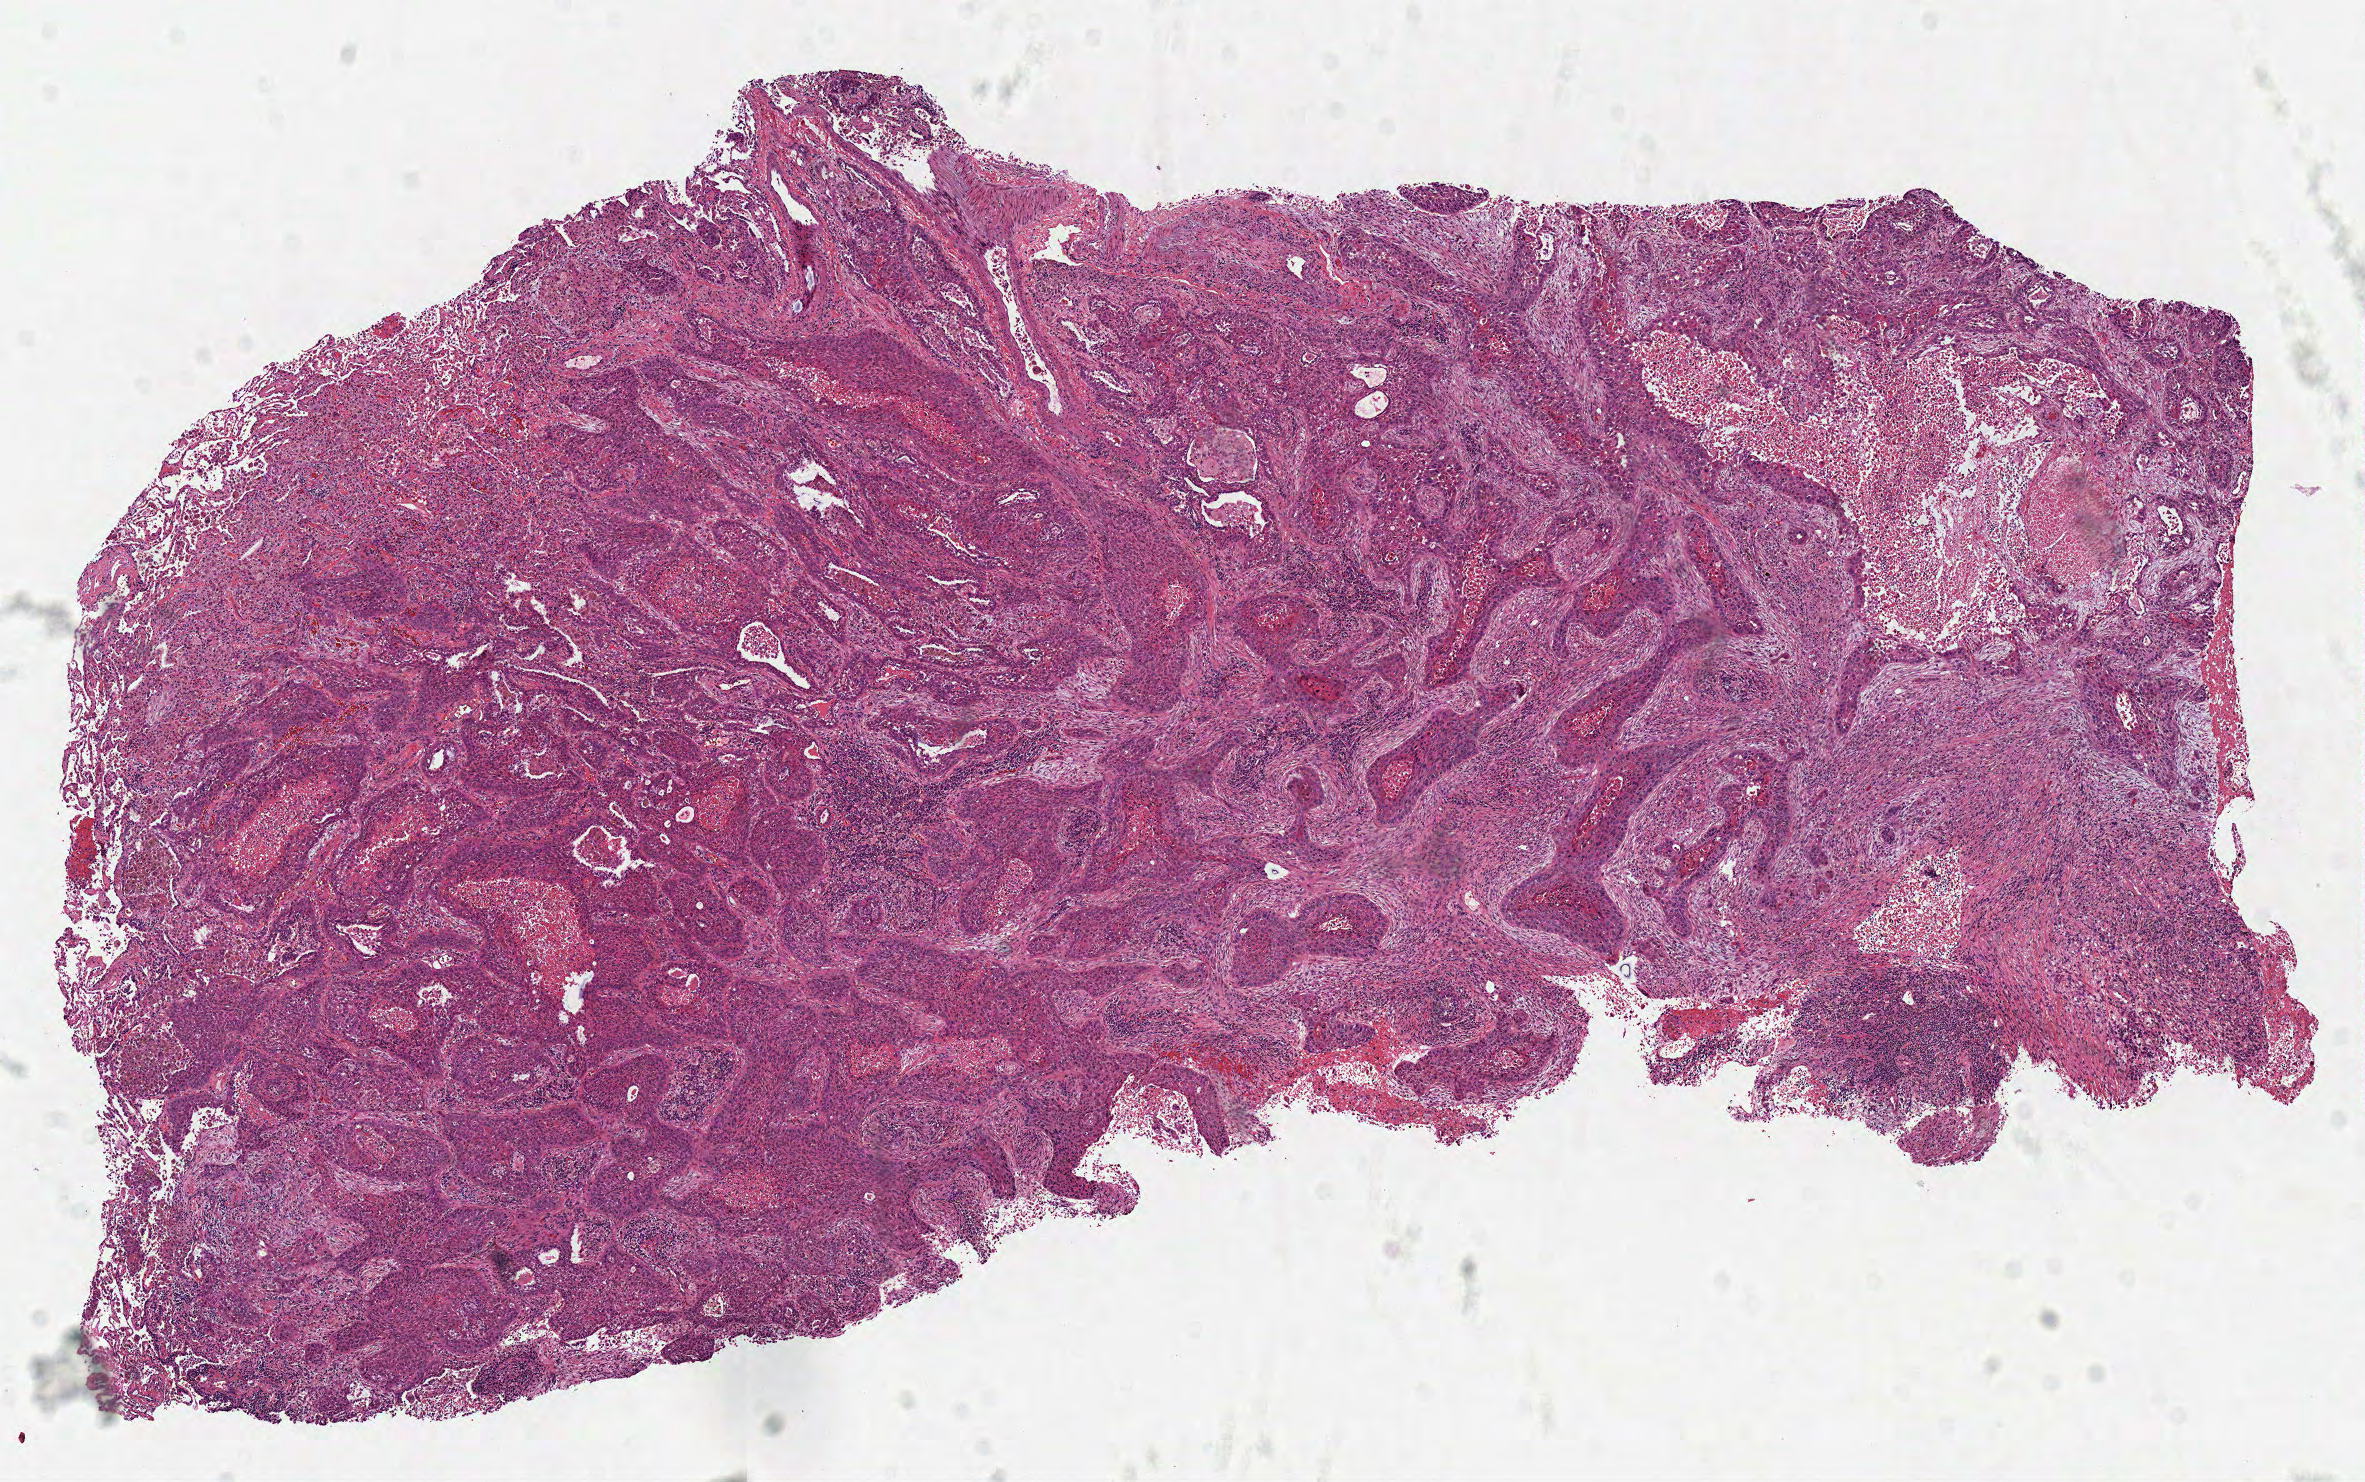
Digitized Hematoxylin and eosin (H&E) stained tissue section (whole slide) — shown as a low-resolution overview of the whole scanned area (about 9.3 x 5.8 mm), frozen section from the top of the tissue portion, primary tumour sample from the lung. Female, age 59 years at initial diagnosis. Composition of this section per pathologist review: tumour cells 85%, tumour nuclei 71%, normal cells 0%, stromal cells 4%, necrosis 11%. Inflammatory infiltration, as recorded: lymphocyte infiltration 20%, monocyte infiltration 2%, neutrophil infiltration 5%.
• AJCC pathologic stage: IB
• pathologic diagnosis: Squamous cell carcinoma, NOS (upper lobe, lung)